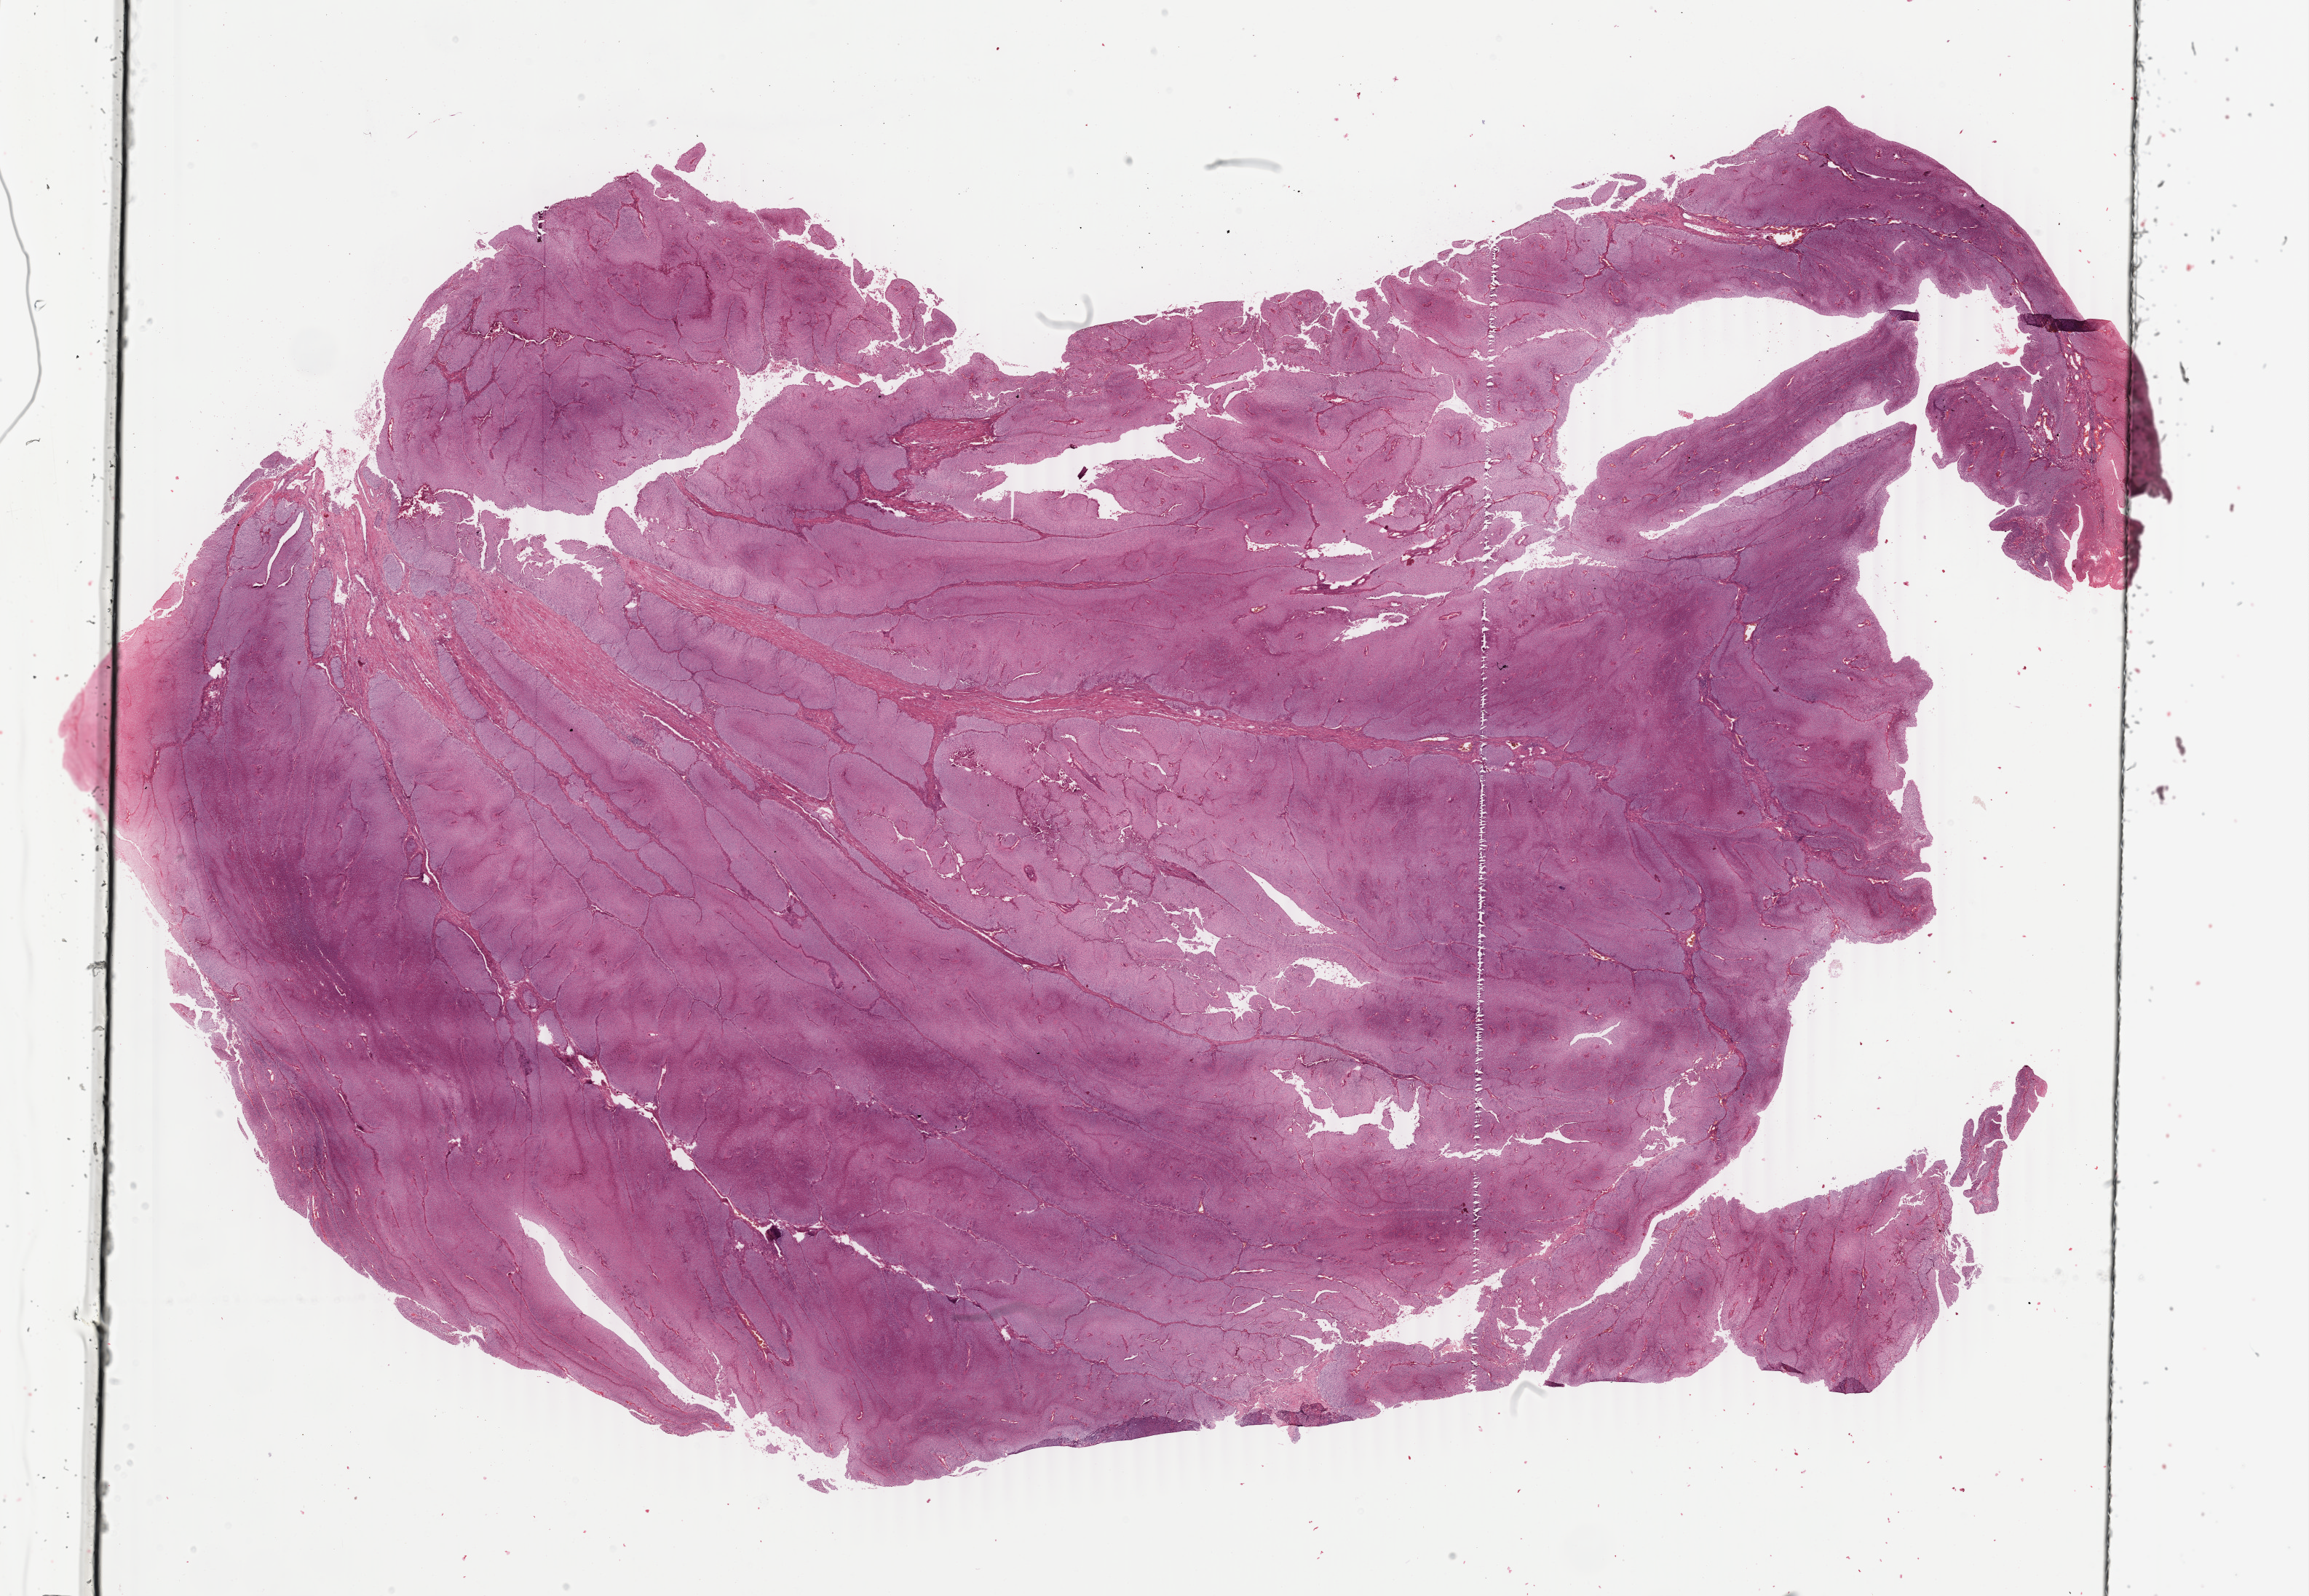
Whole-slide histology image, Hematoxylin and eosin (H&E) stained, a low-resolution overview of the entire scanned area, about 25.2 x 17.4 mm (acquisition: 40x scan). FFPE section. Sample: primary tumour, bladder. Male, age 55 years at initial diagnosis. Histologic grade: low grade.
- AJCC pathologic stage: II (7th edition)
- diagnosis: Papillary transitional cell carcinoma